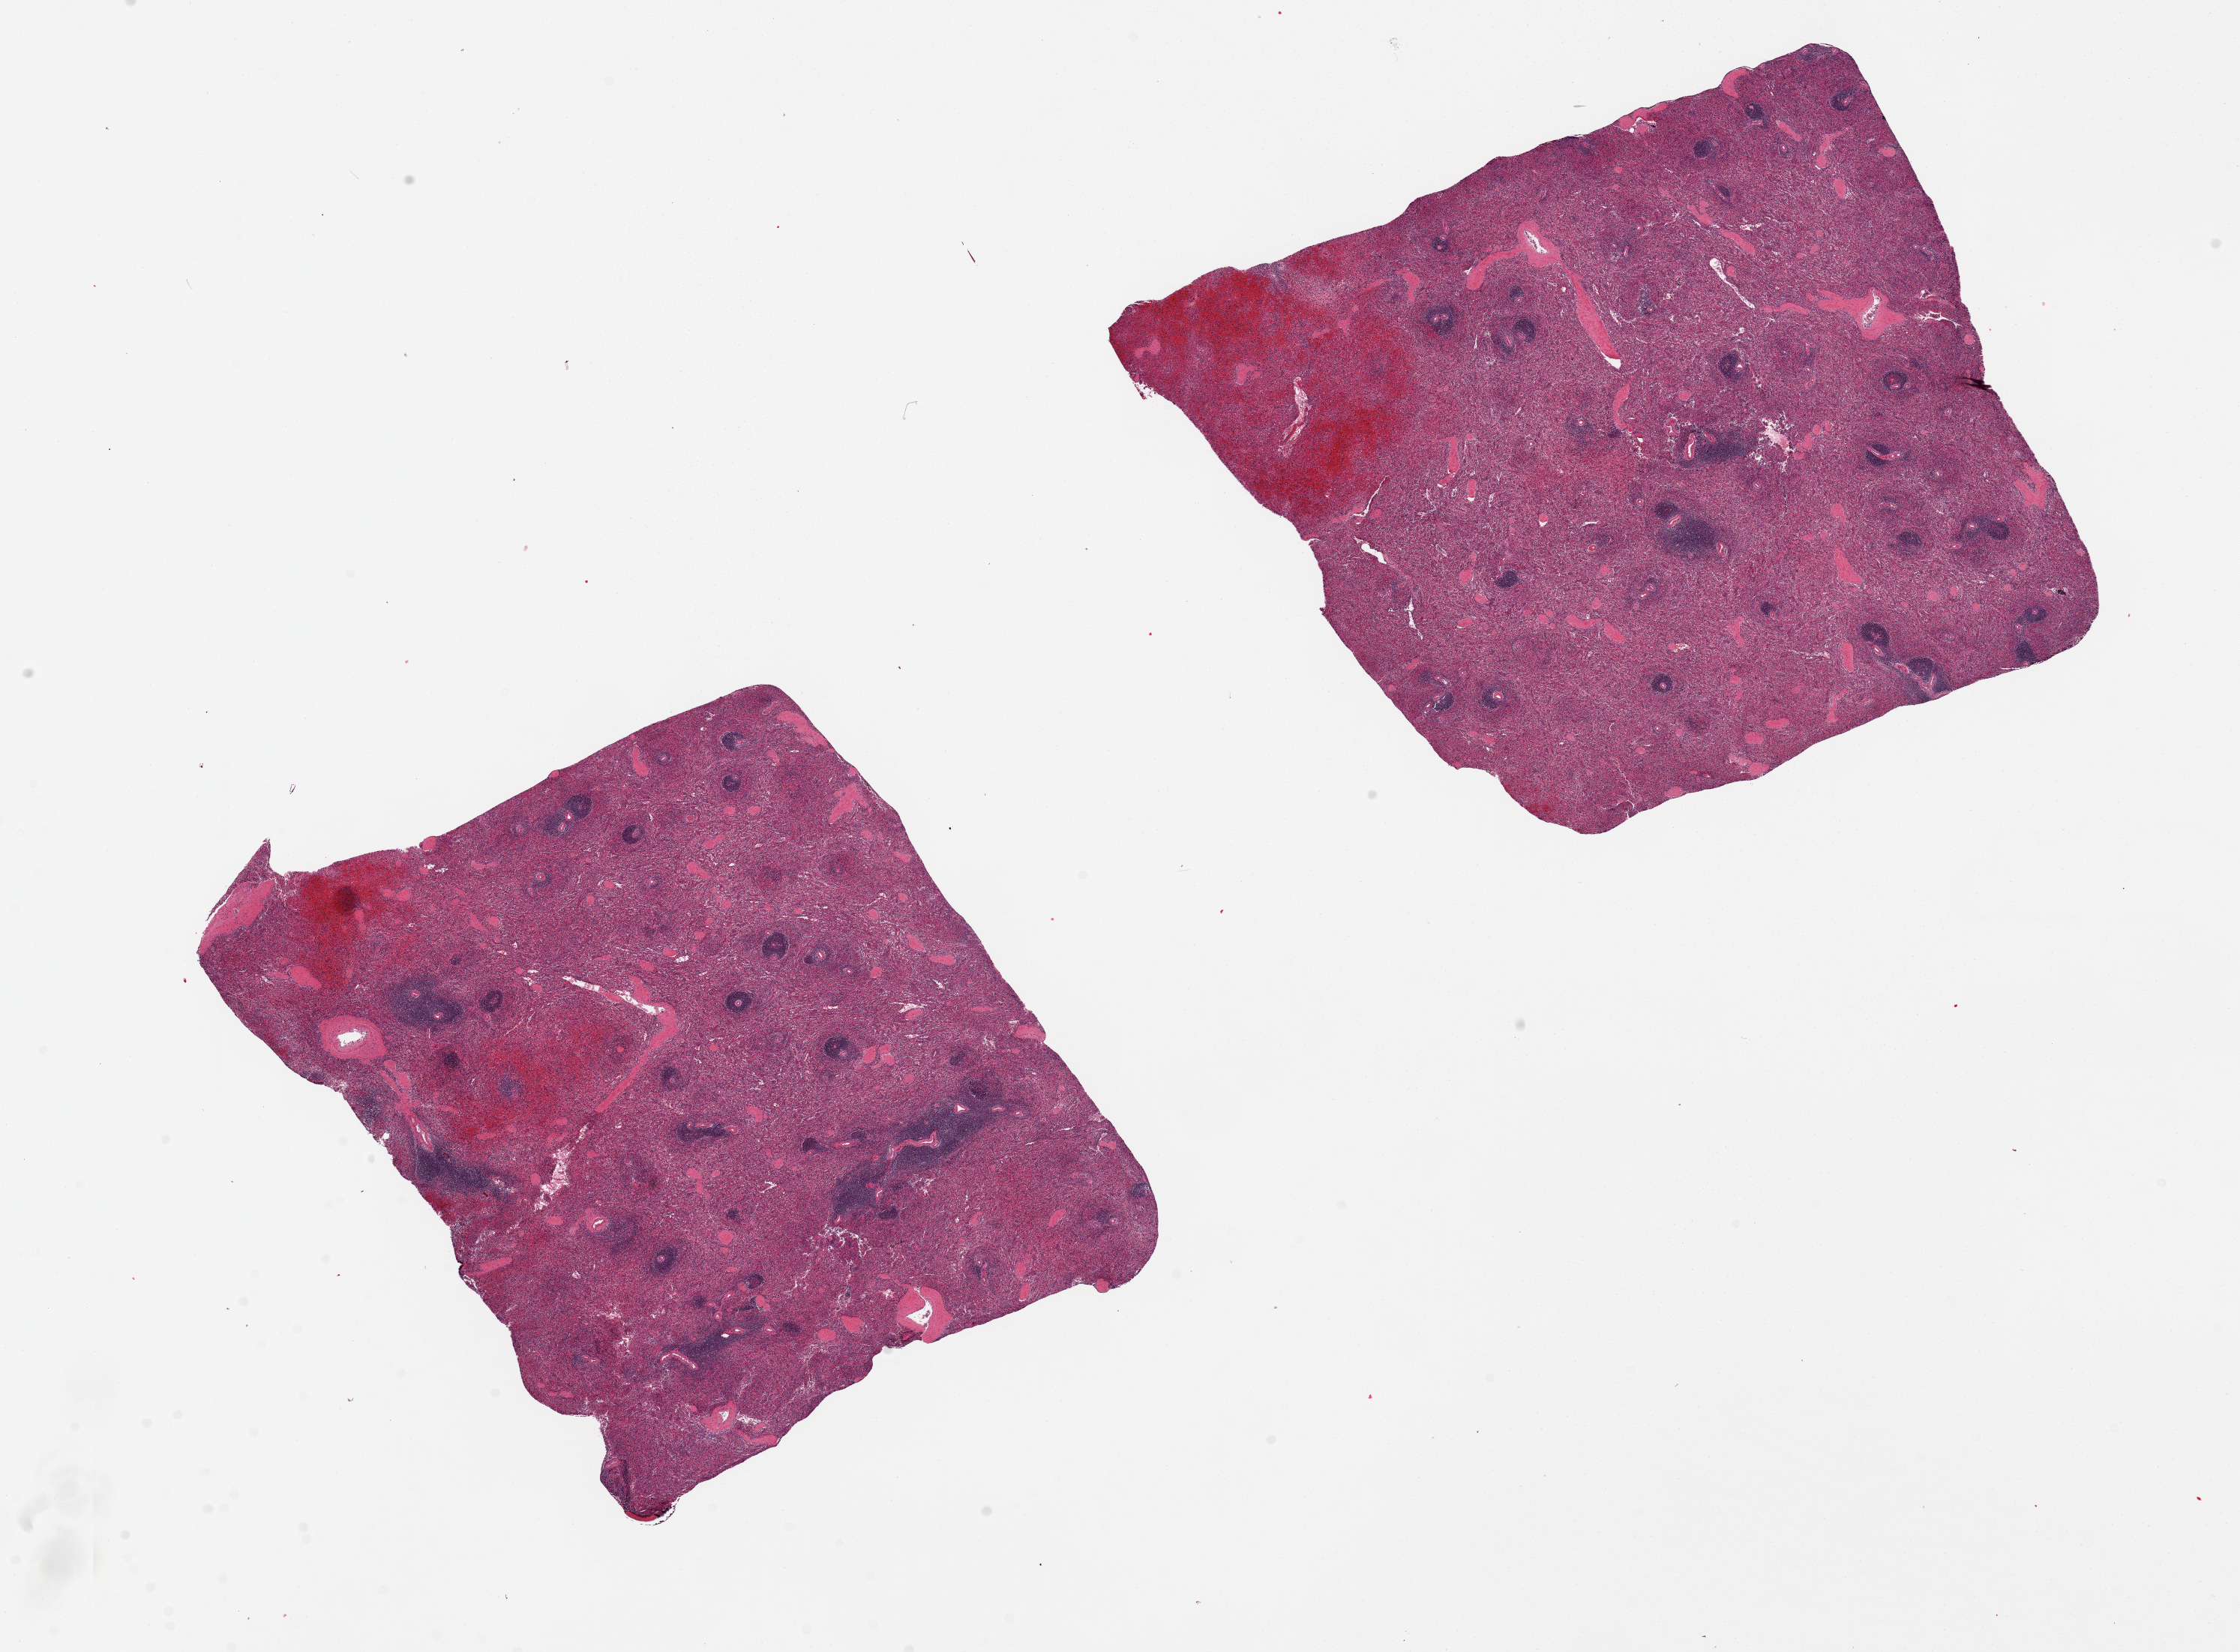
Digitized haematoxylin and eosin-stained section, brightfield, shown as a low-resolution overview of the whole scanned area (about 23.6 x 17.4 mm, acquisition: 20x scan). PAXgene-fixed, paraffin-embedded tissue. Sampled site (target tissue): spleen. Tissue donor sample. Male donor.
Pathologist's review note for this sample: 2 pieces; focal hemorrhages.